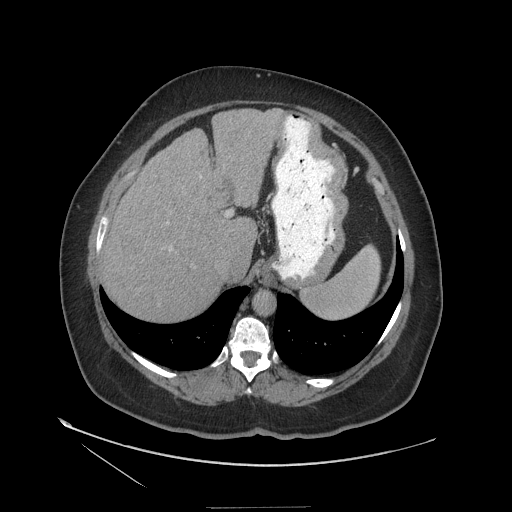
Contrast-enhanced abdominal CT (liver protocol), one axial slice; reconstruction kernel STANDARD; 140 kVp; soft-tissue window (W 400 / L 40 HU); 2.5 mm slice thickness; 512 × 512 image matrix, field of view 480 × 480 mm. Case-level facts recorded for this patient, not image findings: diagnosis: hepatocellular carcinoma (patient treated with transarterial chemoembolisation; whether this scan precedes or follows treatment is not stated here); TNM stage (as recorded): Stage-II; Child-Pugh class: A; tumour nodularity: multinodular; tumour size: 3 cm.
Outlined on this slice (semi-automatically segmented with operator editing):
- abdominal aorta: bounding box [x1, y1, x2, y2] px = [253, 292, 275, 316]
- liver parenchyma outside the tumour (the mass and vessels are separate outlines, so this box may not span the whole liver): [100, 108, 284, 320]
- mass: [119, 233, 148, 259]
- liver vessels: [226, 211, 230, 216]